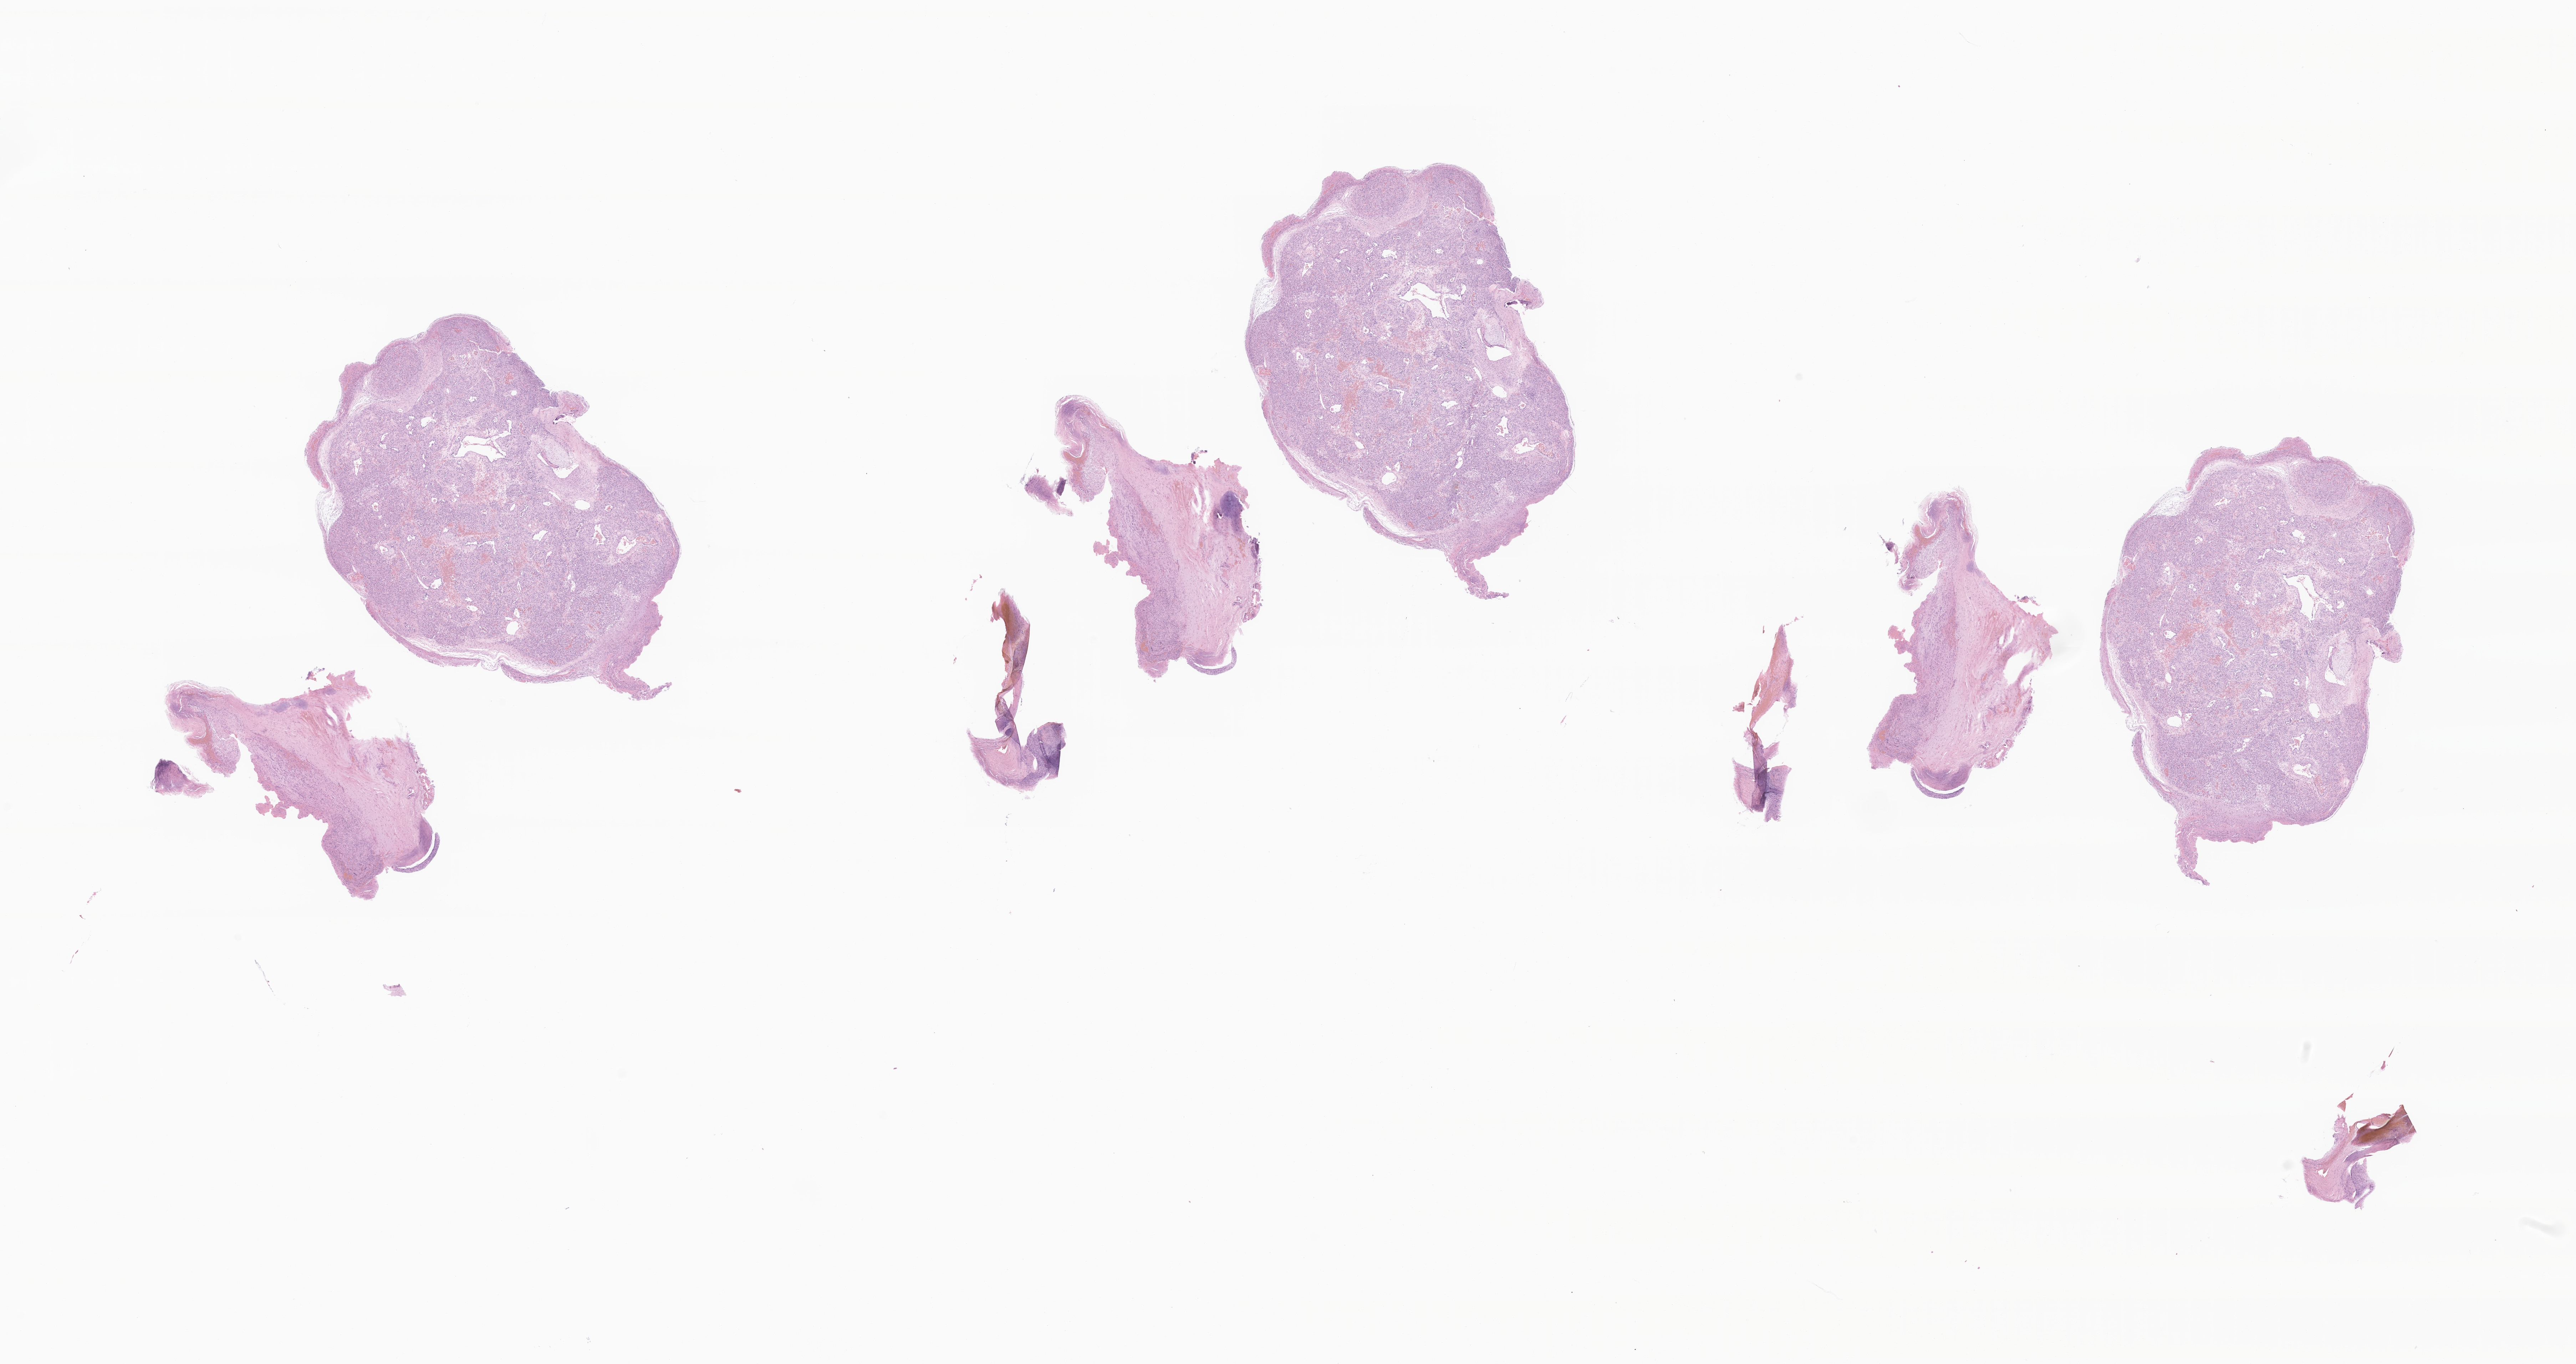
Hematoxylin and eosin (H&E) whole-slide image of tumor tissue from the brain, shown as a low-resolution overview of the whole scanned area (about 30.4 x 16.1 mm). Formalin-fixed paraffin-embedded section. Patient male; age 215 months (17 years 11 months).
- diagnosis: Hemangioma, NOS